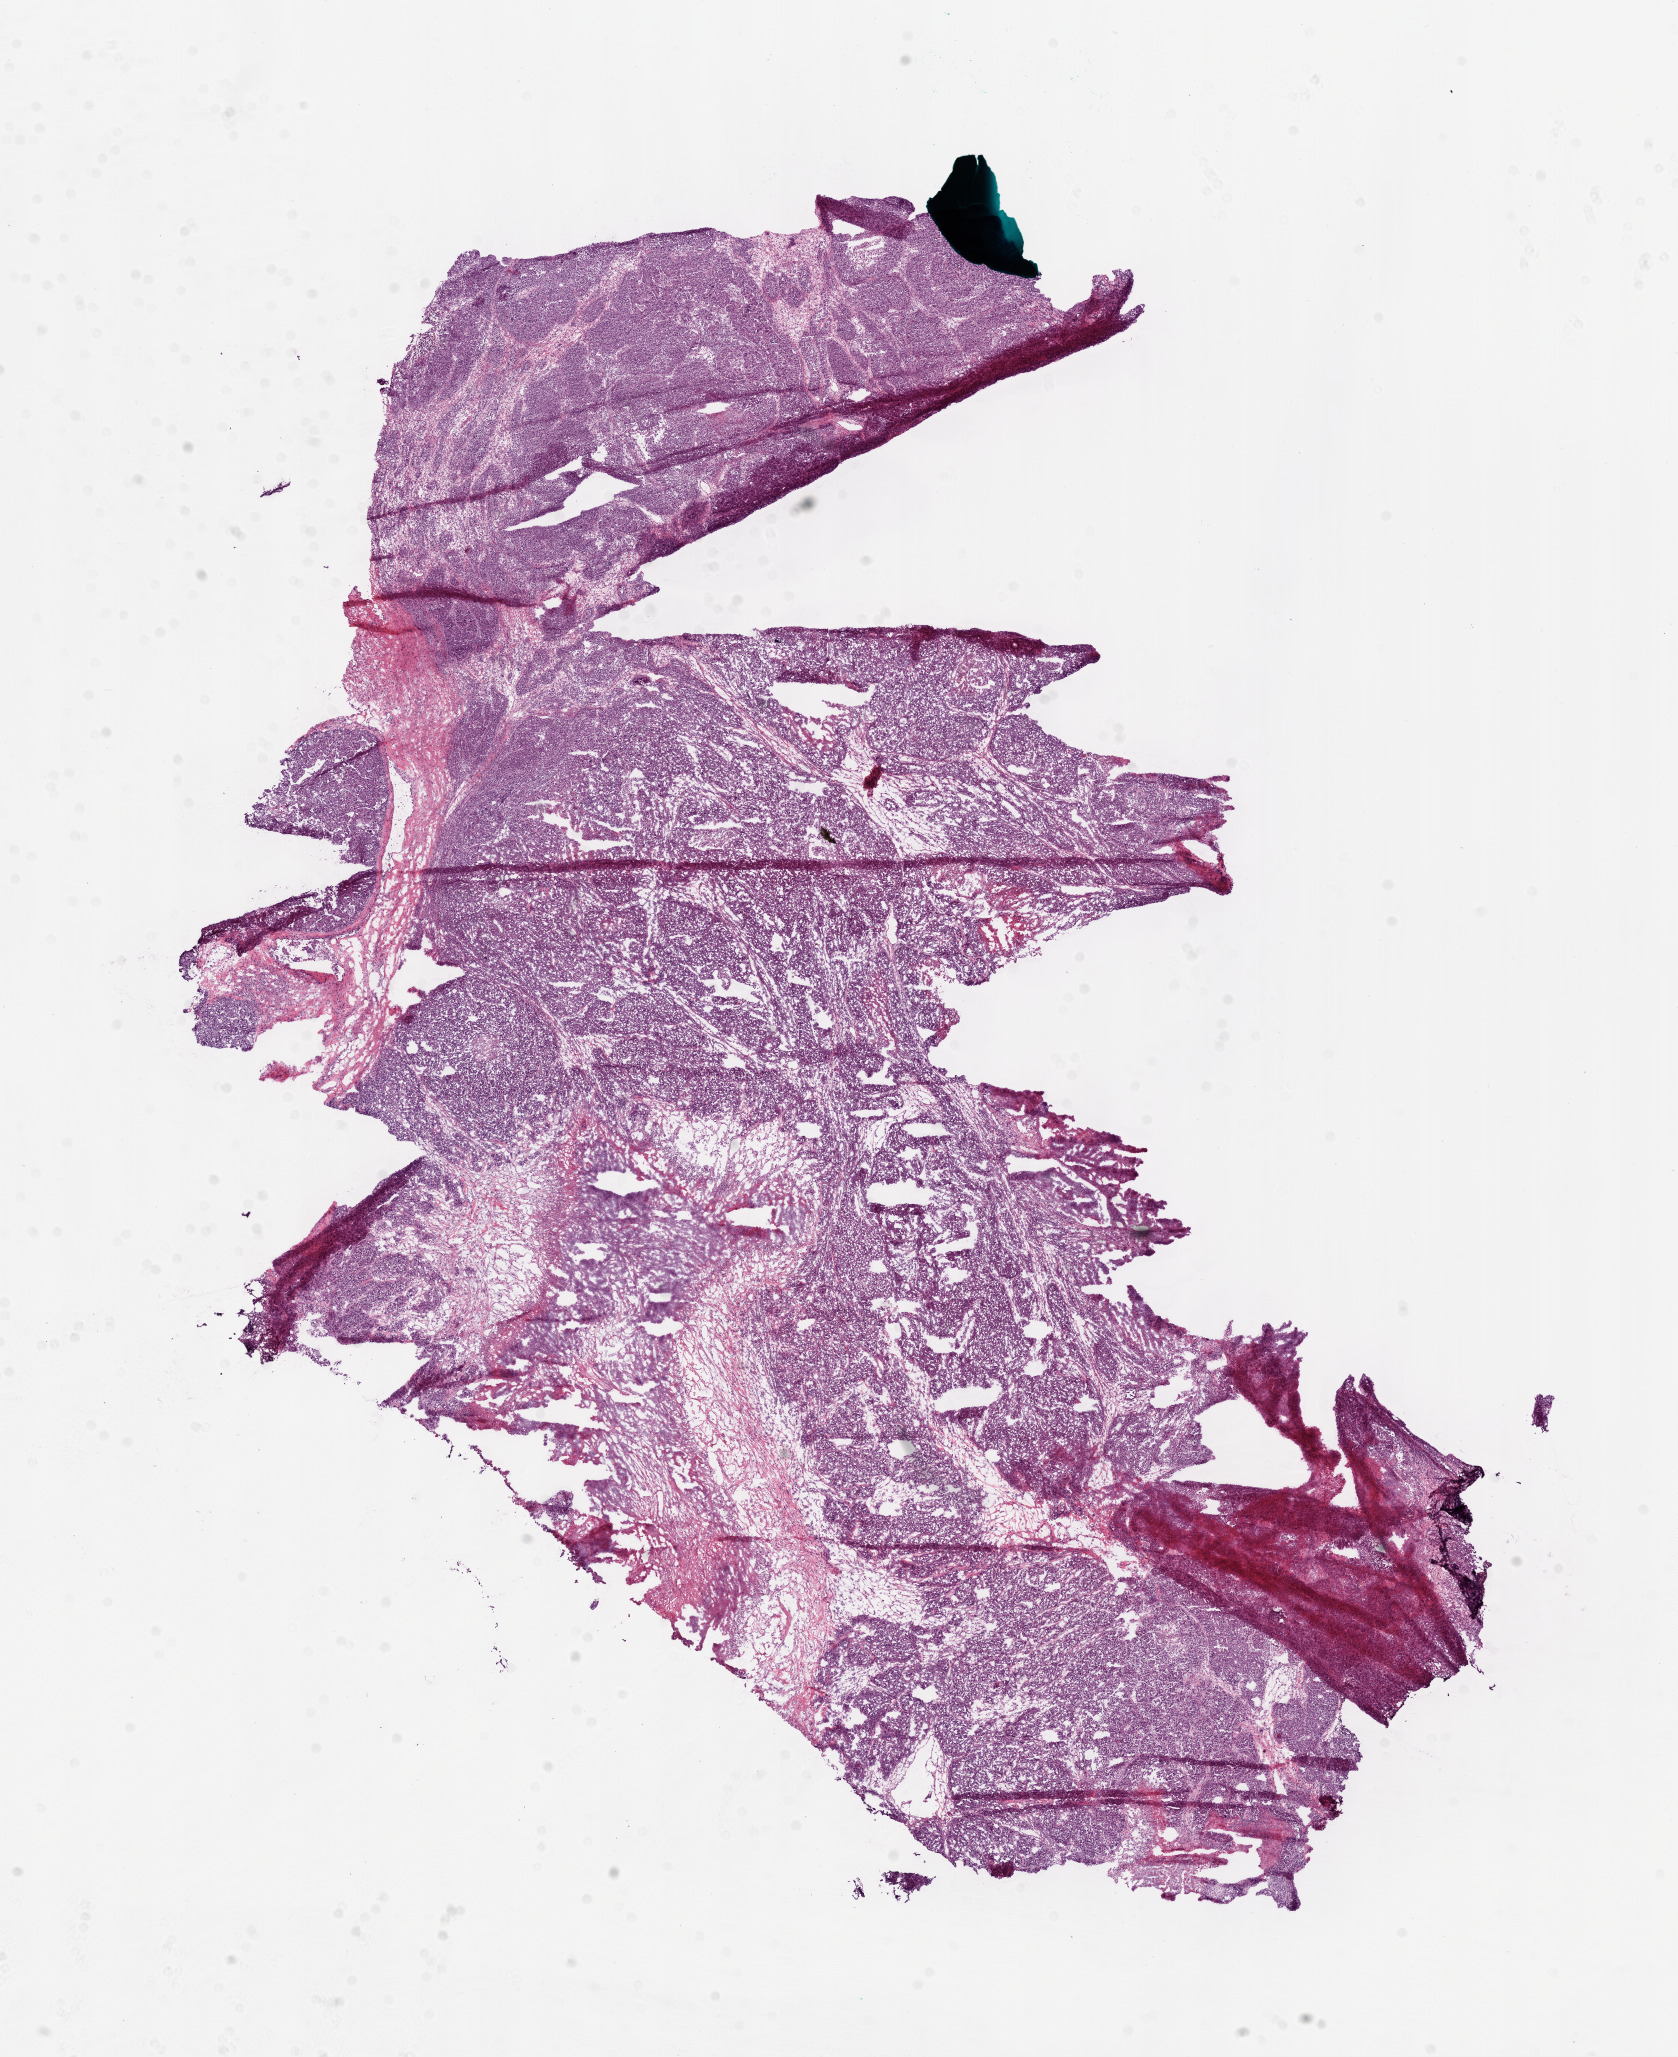
Whole-slide histology image, H&E-stained — whole scanned area (about 13.5 x 16.6 mm) shown as a low-resolution overview. Frozen section. Ovary, primary tumour sample. Female patient; age at initial diagnosis 61 years. Histologic grade: G3 (poorly differentiated). Slide review estimates, as recorded: tumour cells 78%, tumour nuclei 80%, normal cells 18%, stromal cells 2%, necrosis 2%.
Diagnosis: Serous cystadenocarcinoma, NOS. Laterality: bilateral. FIGO stage: IIIC.